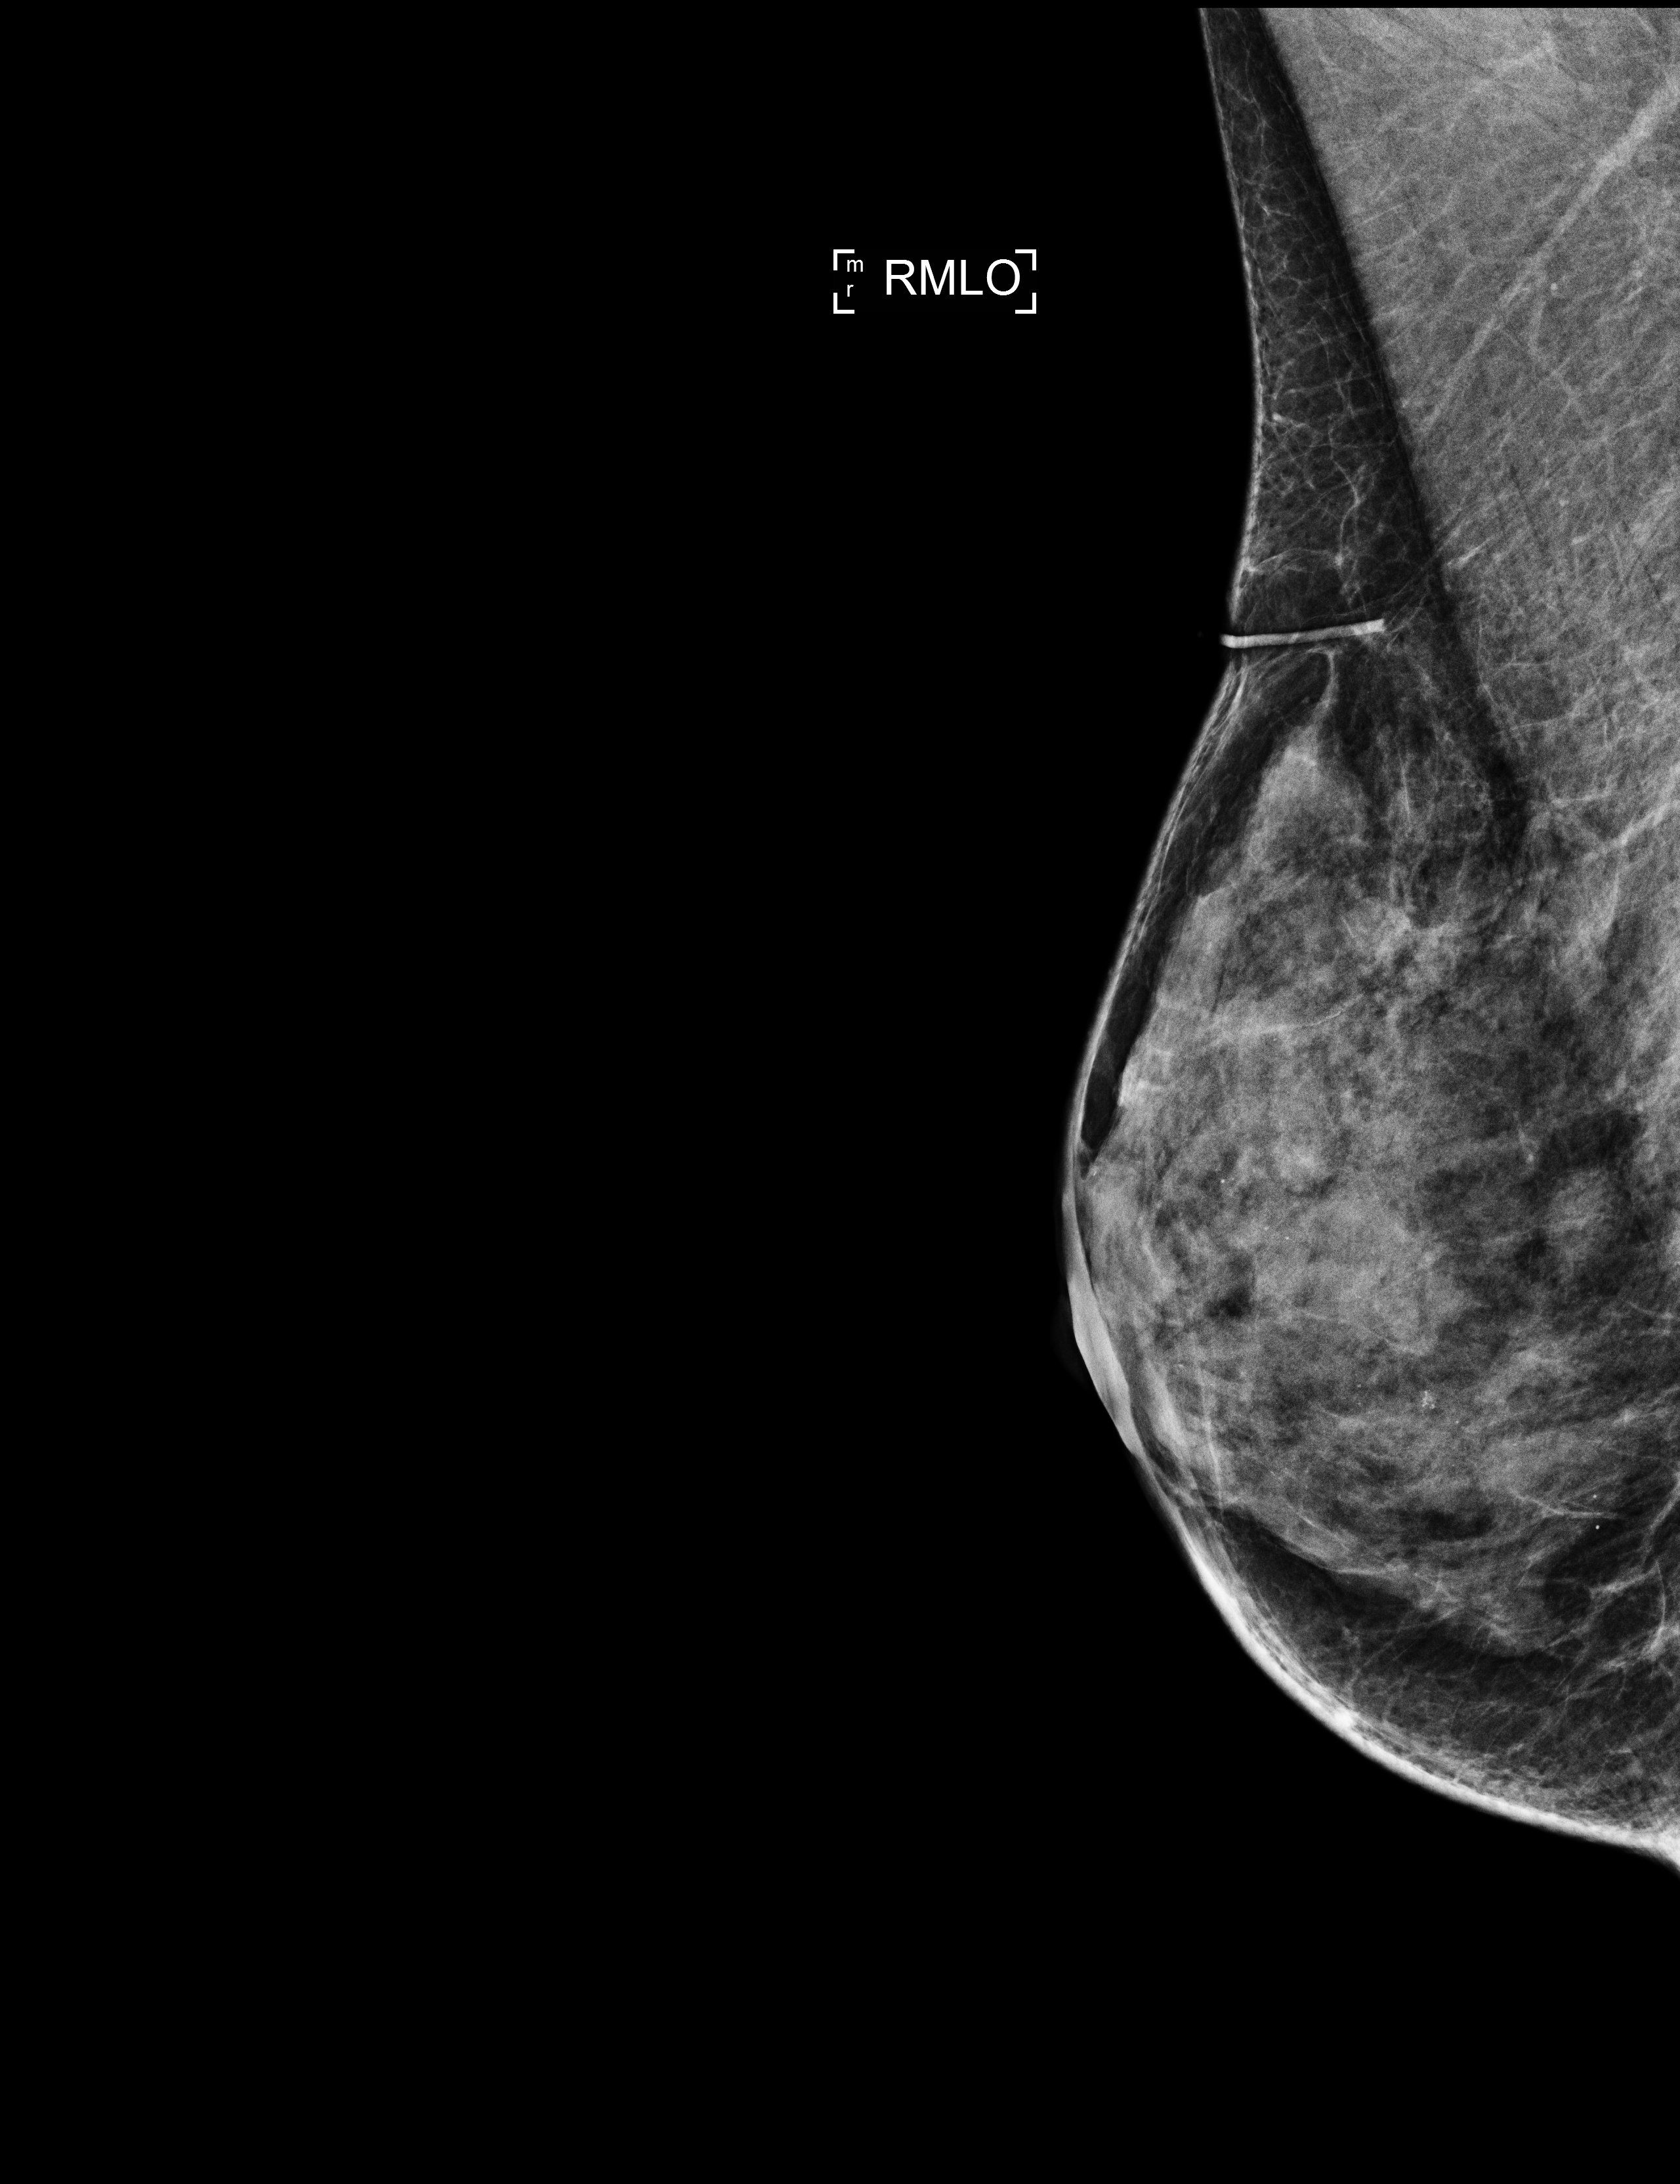
Digital mammogram (FFDM); right breast; medio-lateral oblique projection; screening examination. Patient aged 50 years (female).
Breast density at the screening exam (both breasts): extremely dense (BI-RADS density category d). Final BI-RADS assessment for this screening round (tomosynthesis exam, both breasts): category 3. Recall: recalled for additional imaging after this screen.